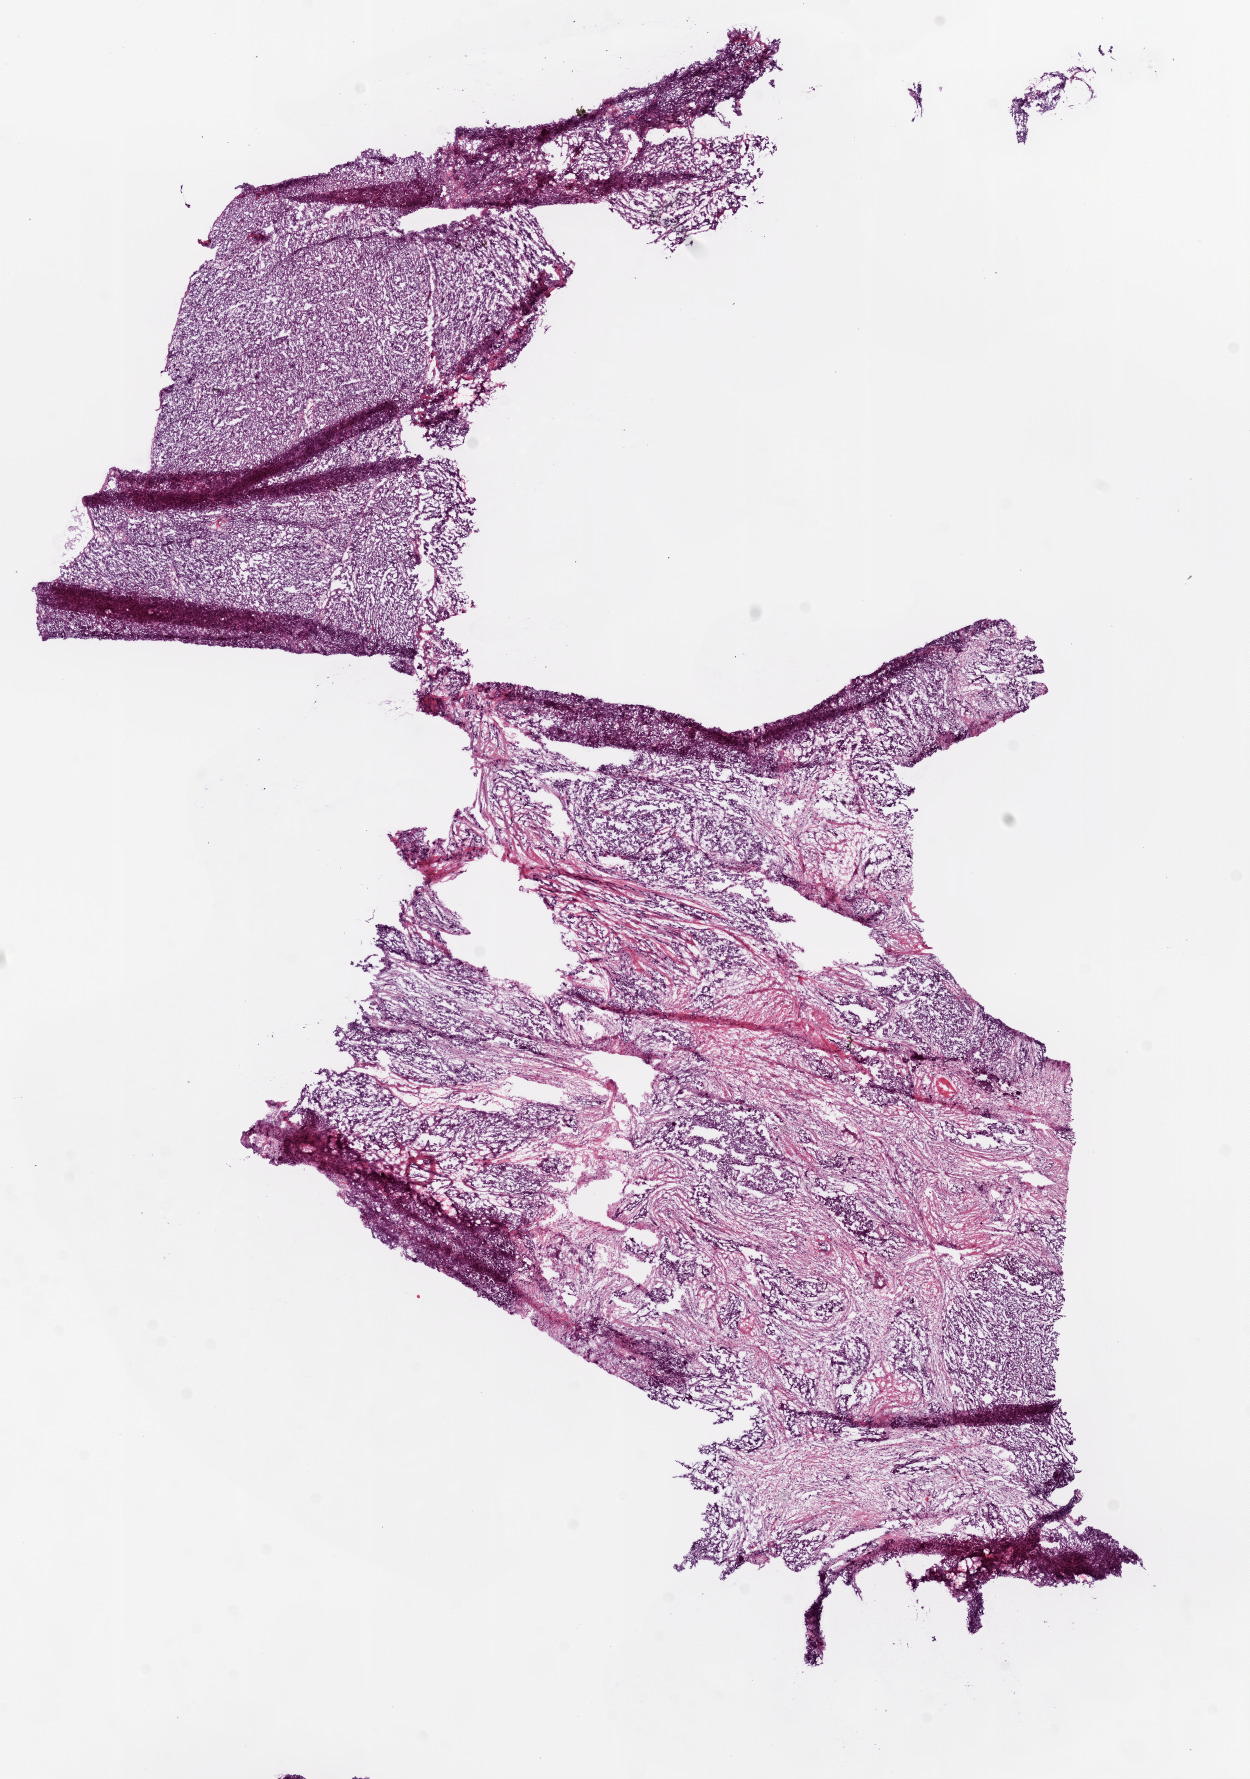
Whole-slide histology image, H&E-stained, whole scanned area (about 10.0 x 14.3 mm) shown as a low-resolution overview; frozen section from the bottom of the tissue portion; primary tumour sample from the ovary. Patient: female, age at initial diagnosis 55 years. Histologic grade: G3 (poorly differentiated). Slide review estimates, as recorded: tumour cells 85%, tumour nuclei 80%, normal cells 0%, stromal cells 15%, necrosis 0%.
* FIGO stage: IIIC
* pathologic diagnosis: Serous cystadenocarcinoma, NOS